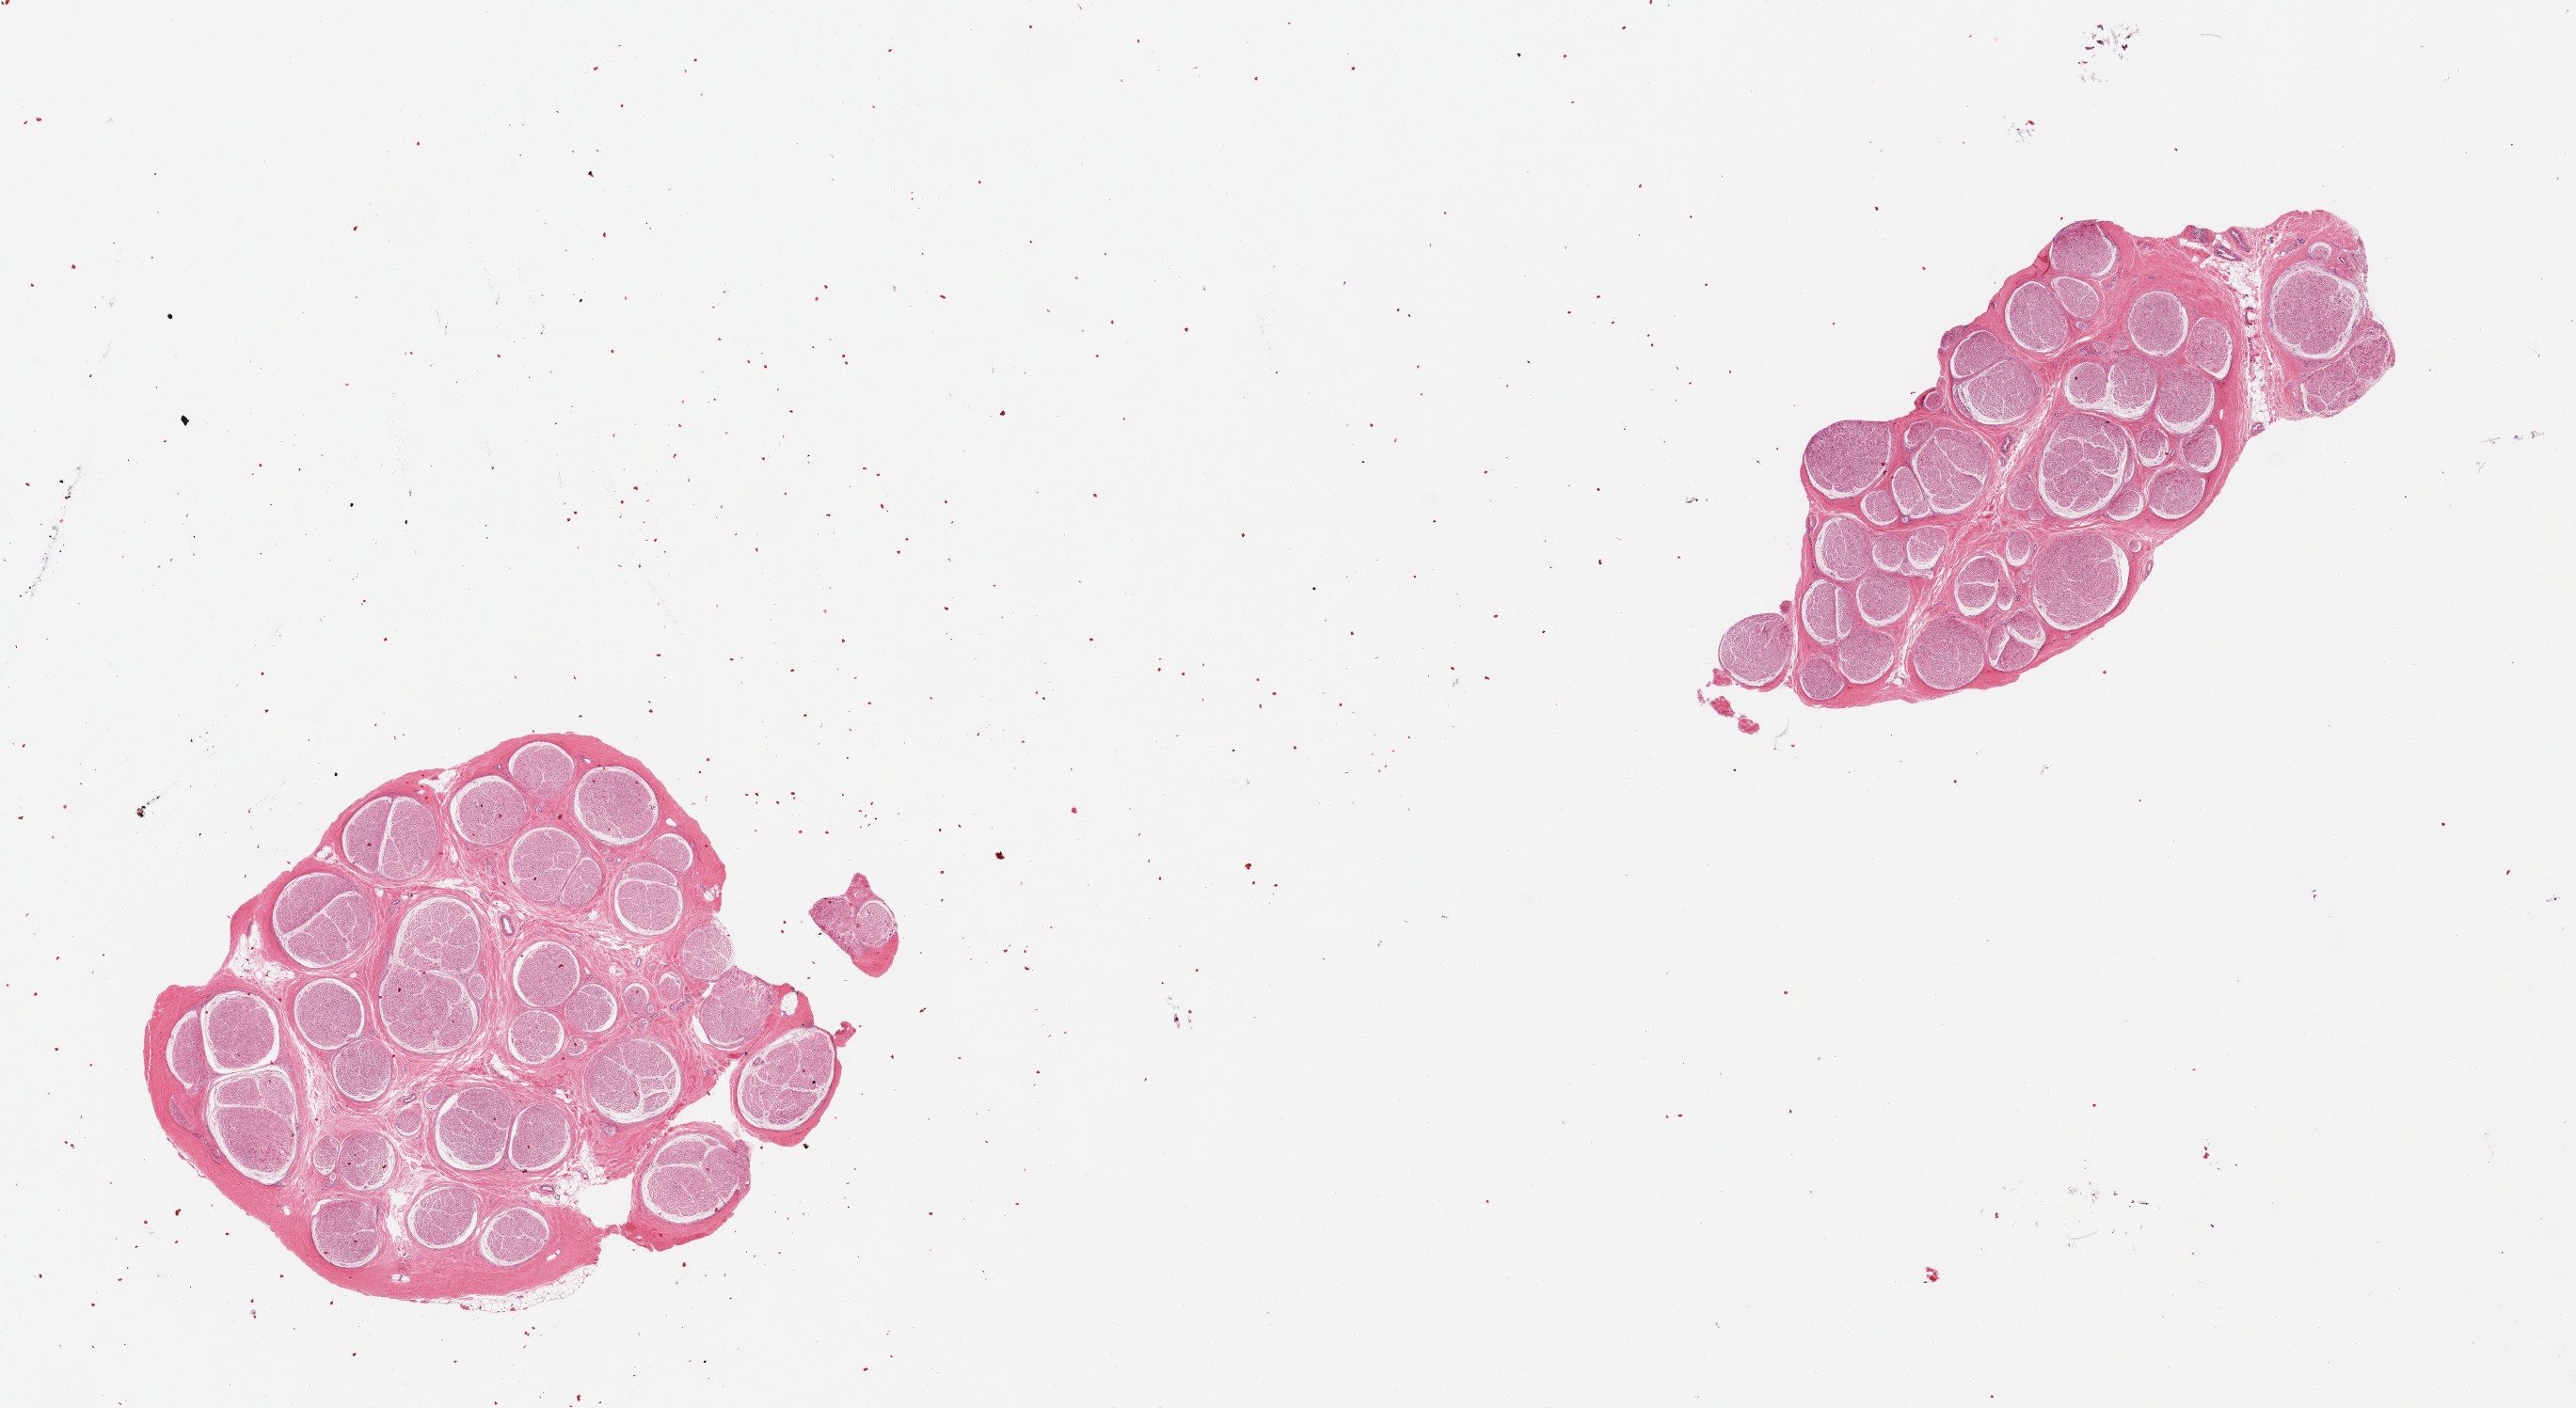
Hematoxylin and eosin (H&E) whole-slide image — shown as a low-resolution overview of the whole scanned area (about 21.7 x 11.8 mm); PAXgene-fixed, paraffin-embedded tissue; sampled site (target tissue): tibial nerve; donor tissue sample. Donor sex: female.
Pathologist's review note for this sample: 2 pieces.